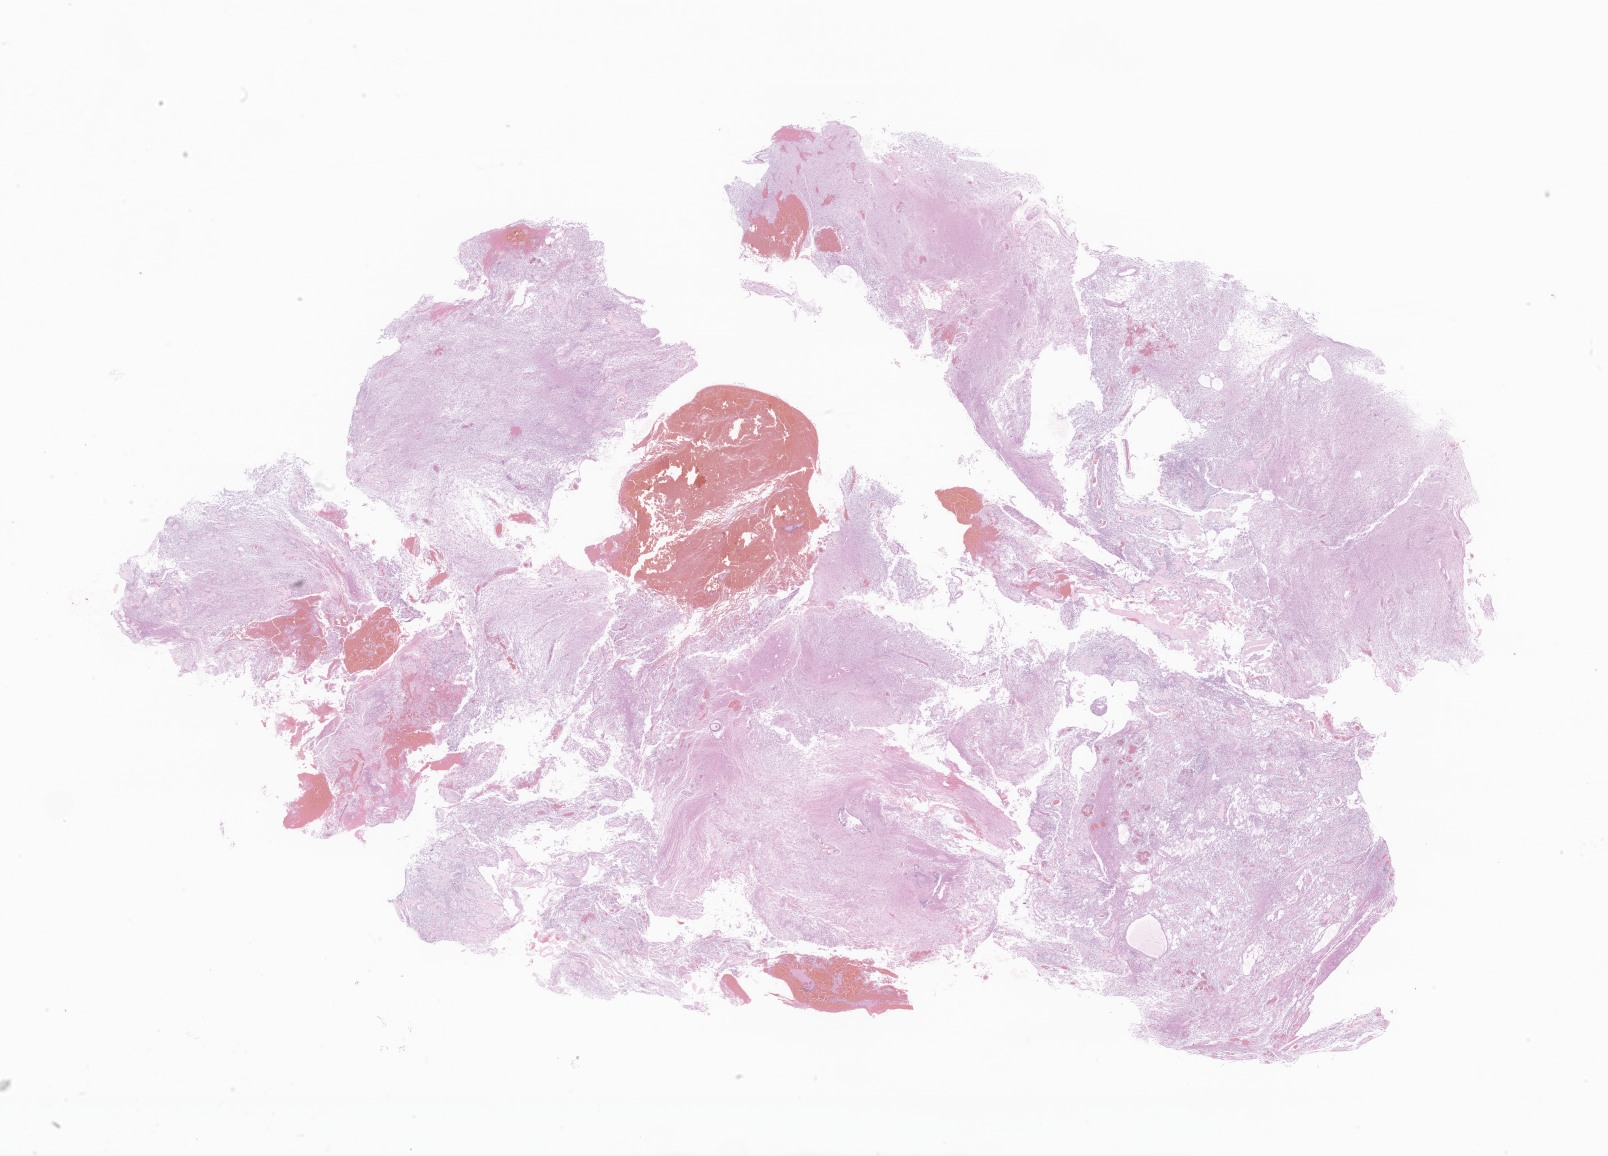
Digitized haematoxylin and eosin-stained section of tumor tissue from the spinal cord — low-resolution overview of the scanned area, about 27.1 x 19.5 mm. Formalin-fixed, paraffin-embedded (FFPE) tissue. Patient female; age 46 months (3 years 10 months).
• recorded diagnosis: Pilocytic astrocytoma